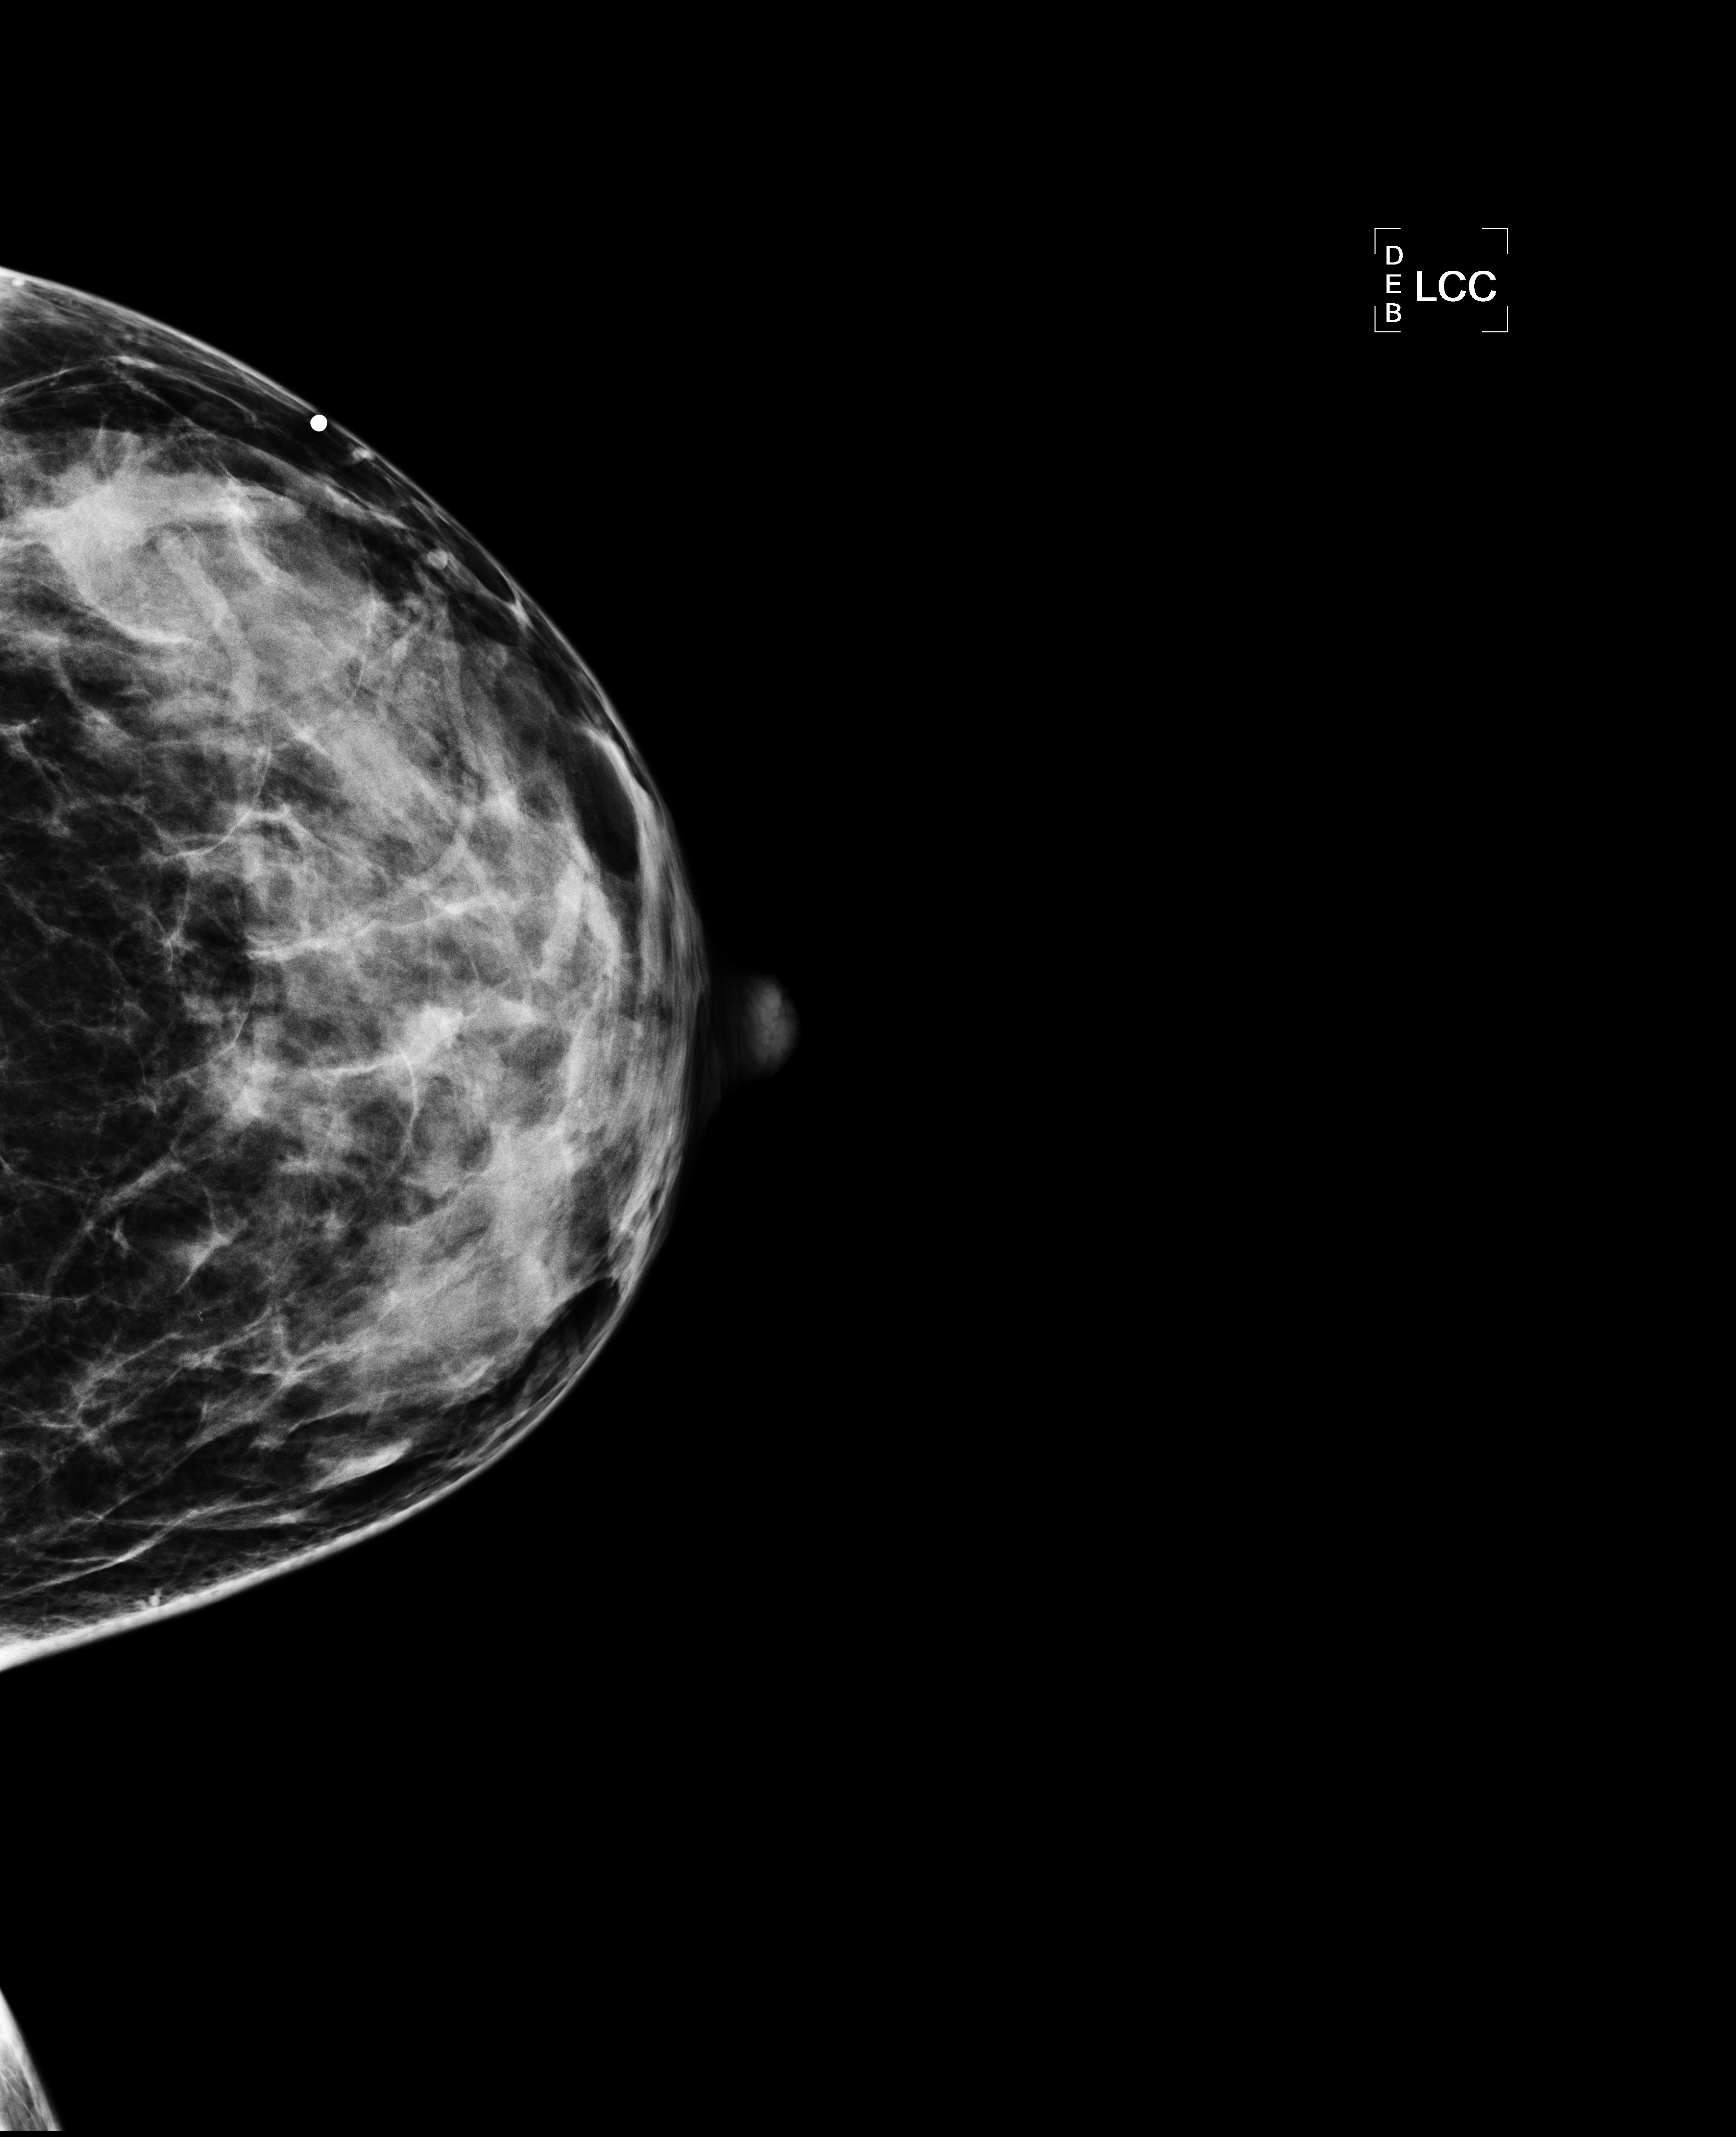
Mammogram, left breast, CC view.
Pathology recorded for this patient (not read from this image): pathology diagnosis: INVASIVE DUCTAL CARCINOMA, MODIFIED SCARFF-BLOOM-RICHARDSON GRADE-I/III. A LESS THAN 5% INTRADUCTAL CARCINOMA COMPONENT, NUCLEAR GRADE-II/III, IS ALSO PRESENT. (left breast); receptor status (as recorded): ER pos (strong), PR pos (strong), HER2 pos; Ki-67 (as recorded): intermed prolif; pathology report notes: mastectomy; INVASIVE DUCTAL CARCINOMA, MODIFIED SCARFF-BLOOM-RICHARDSON GRADE-I/III. A LESS THAN 5% INTRADUCTAL CARCINOMA COMPONENT, NUCLEAR GRADE-II/III, IS ALSO PRESENT; clinical background (as recorded): early 40s with left breast cancer. LMP unknown.